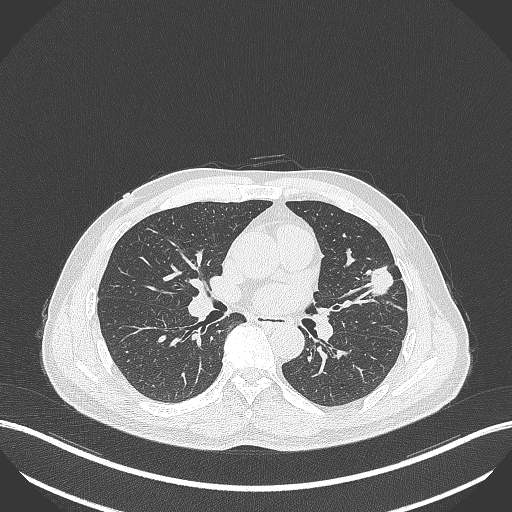
Chest CT, one axial slice. Reconstruction kernel B70f. 120 kVp. Lung window (W 1500 / L -600 HU). 512 × 512 image matrix, field of view 400 × 400 mm. Patient: male, 55 years. Case-level facts recorded for this patient, not image findings: clinical TNM (as recorded): T1c N0 M0; histopathological grade: G2-3.
Structures marked on this image (bounding box drawn by a radiologist):
- lung tumour (recorded histology: adenocarcinoma): bounding box [x1, y1, x2, y2] px = [366, 264, 398, 298]